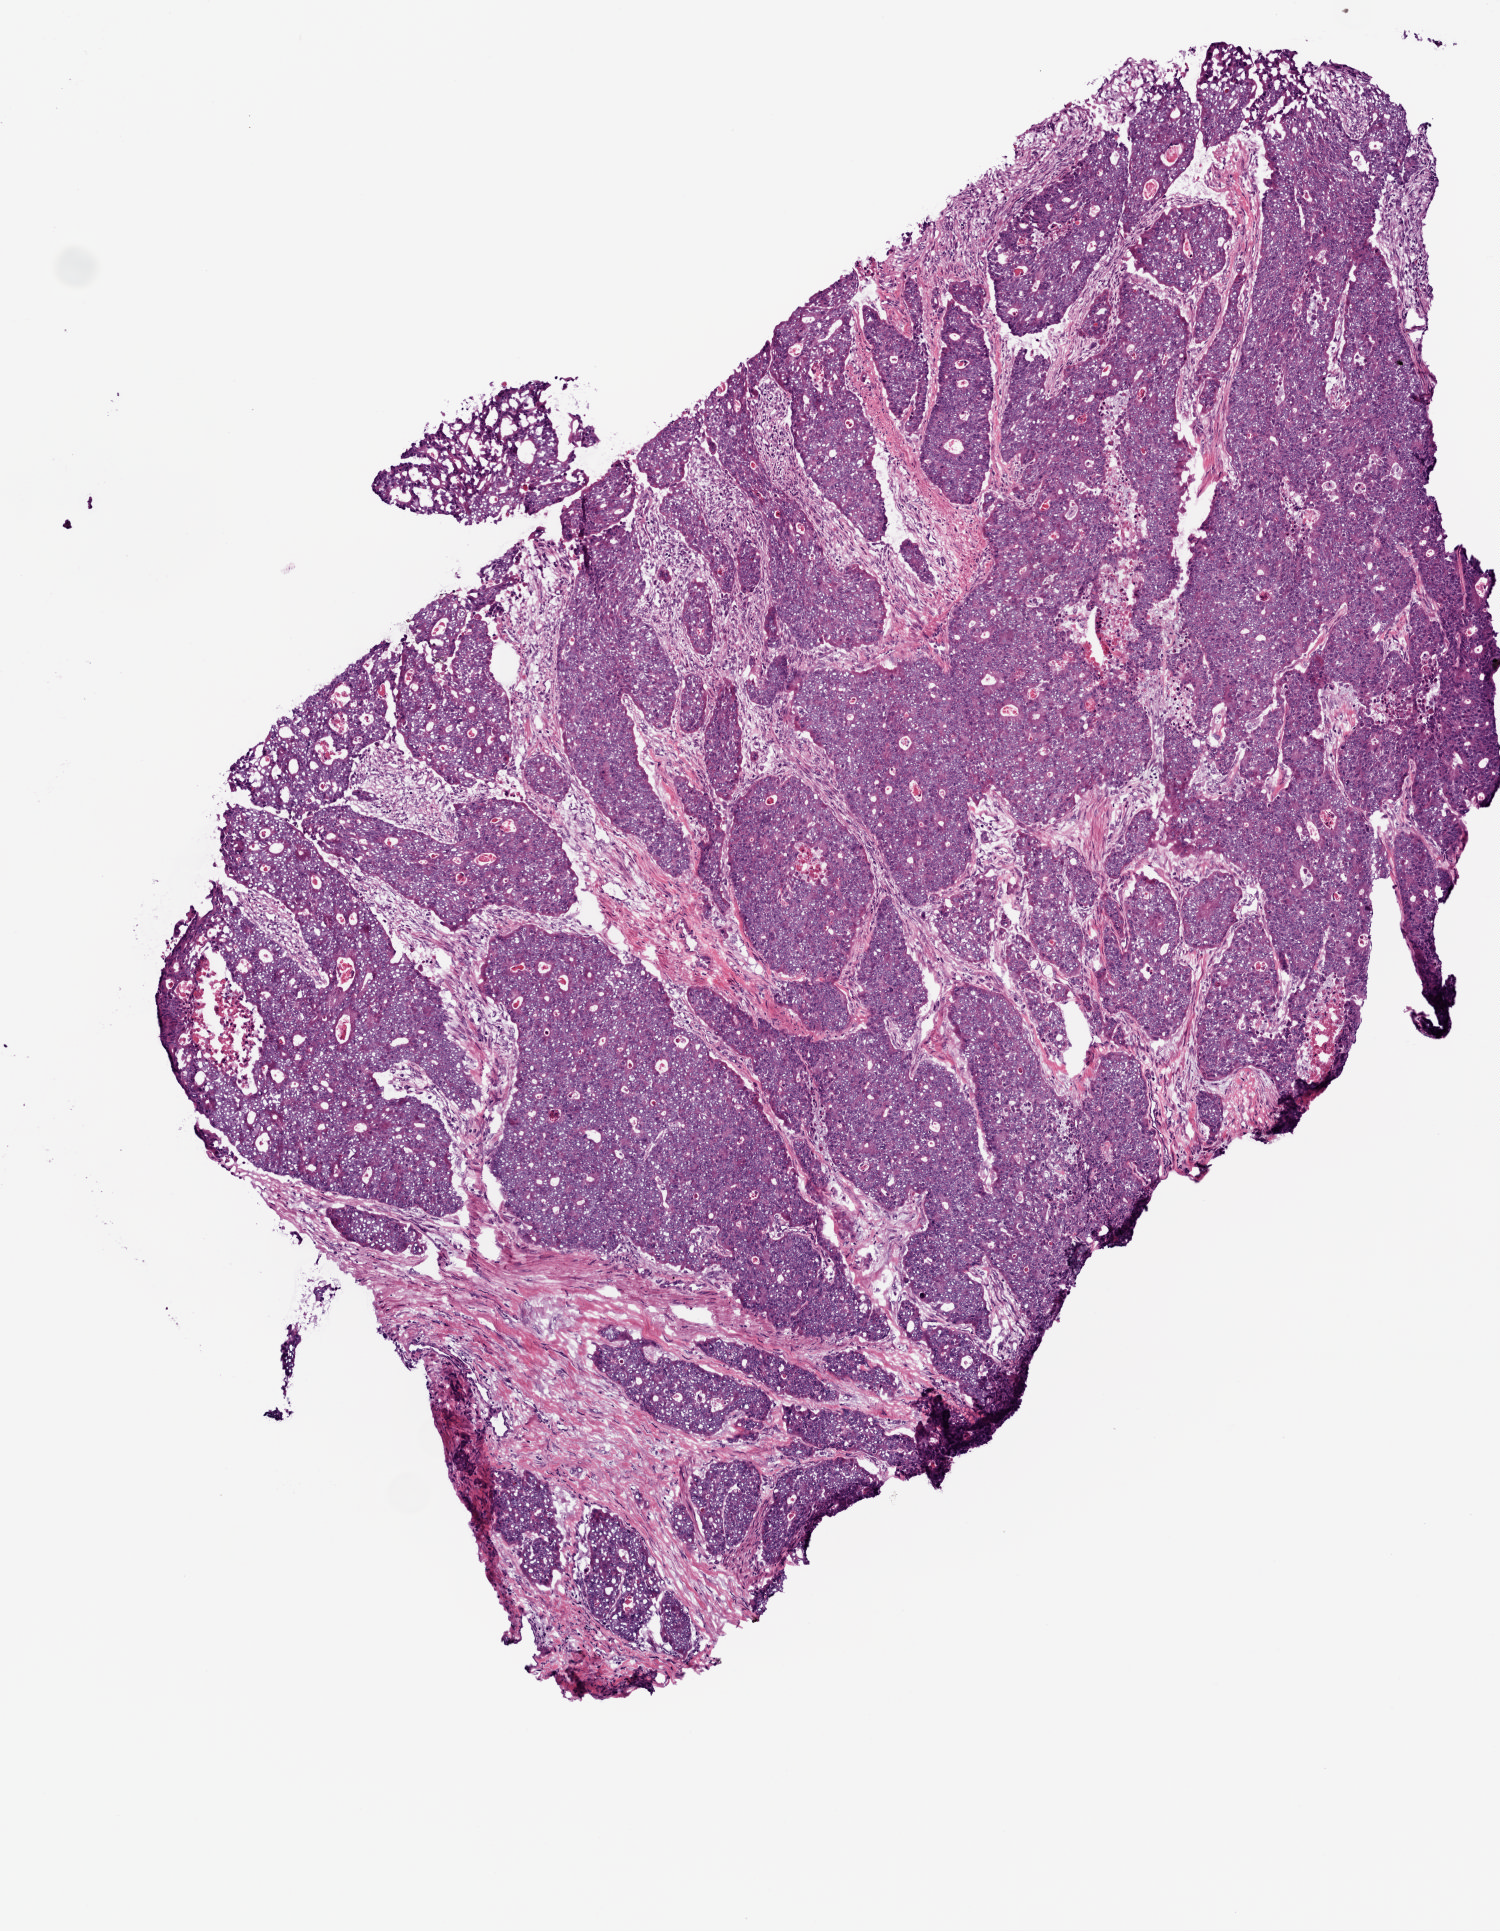
Whole-slide histology image, H&E-stained — shown as a low-resolution overview of the whole scanned area (about 3.0 x 3.9 mm, acquisition: 20x scan); frozen section from the bottom of the tissue portion; primary tumour sample from the colon. Male patient; age at initial diagnosis 46 years. Composition of this section per pathologist review: tumour cells 97%, tumour nuclei 90%, normal cells 0%, stromal cells 0%, necrosis 3%. Infiltration values recorded for this section: lymphocyte infiltration 5%, monocyte infiltration 1%, neutrophil infiltration 2%.
AJCC pathologic stage: IVA. Diagnosis: Adenocarcinoma, NOS (splenic flexure of colon). Lymph nodes positive (case pathology): 7 of 13 examined.